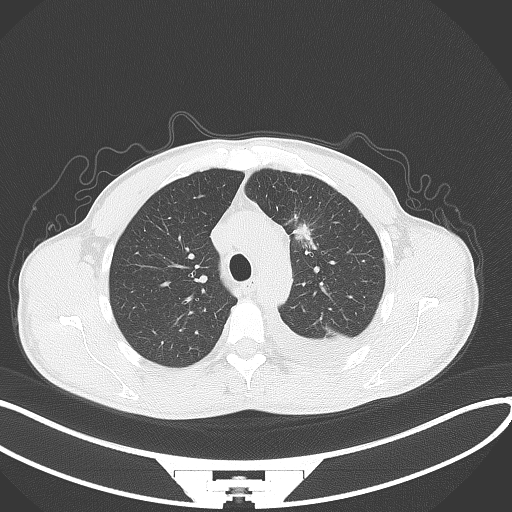
Chest CT, one axial slice; slice 95 of 130 in the series (ordered by position); reconstruction kernel B70f; lung window (W 1500 / L -600 HU); 512 × 512 image matrix. Patient: male, 49 years. From the clinical record (not read from this slice): clinical TNM (as recorded): T1c N1 M1.
Structures marked on this image (bounding box drawn by a radiologist):
- lung tumour (recorded histology: adenocarcinoma): bounding box [x1, y1, x2, y2] px = [285, 212, 319, 257]